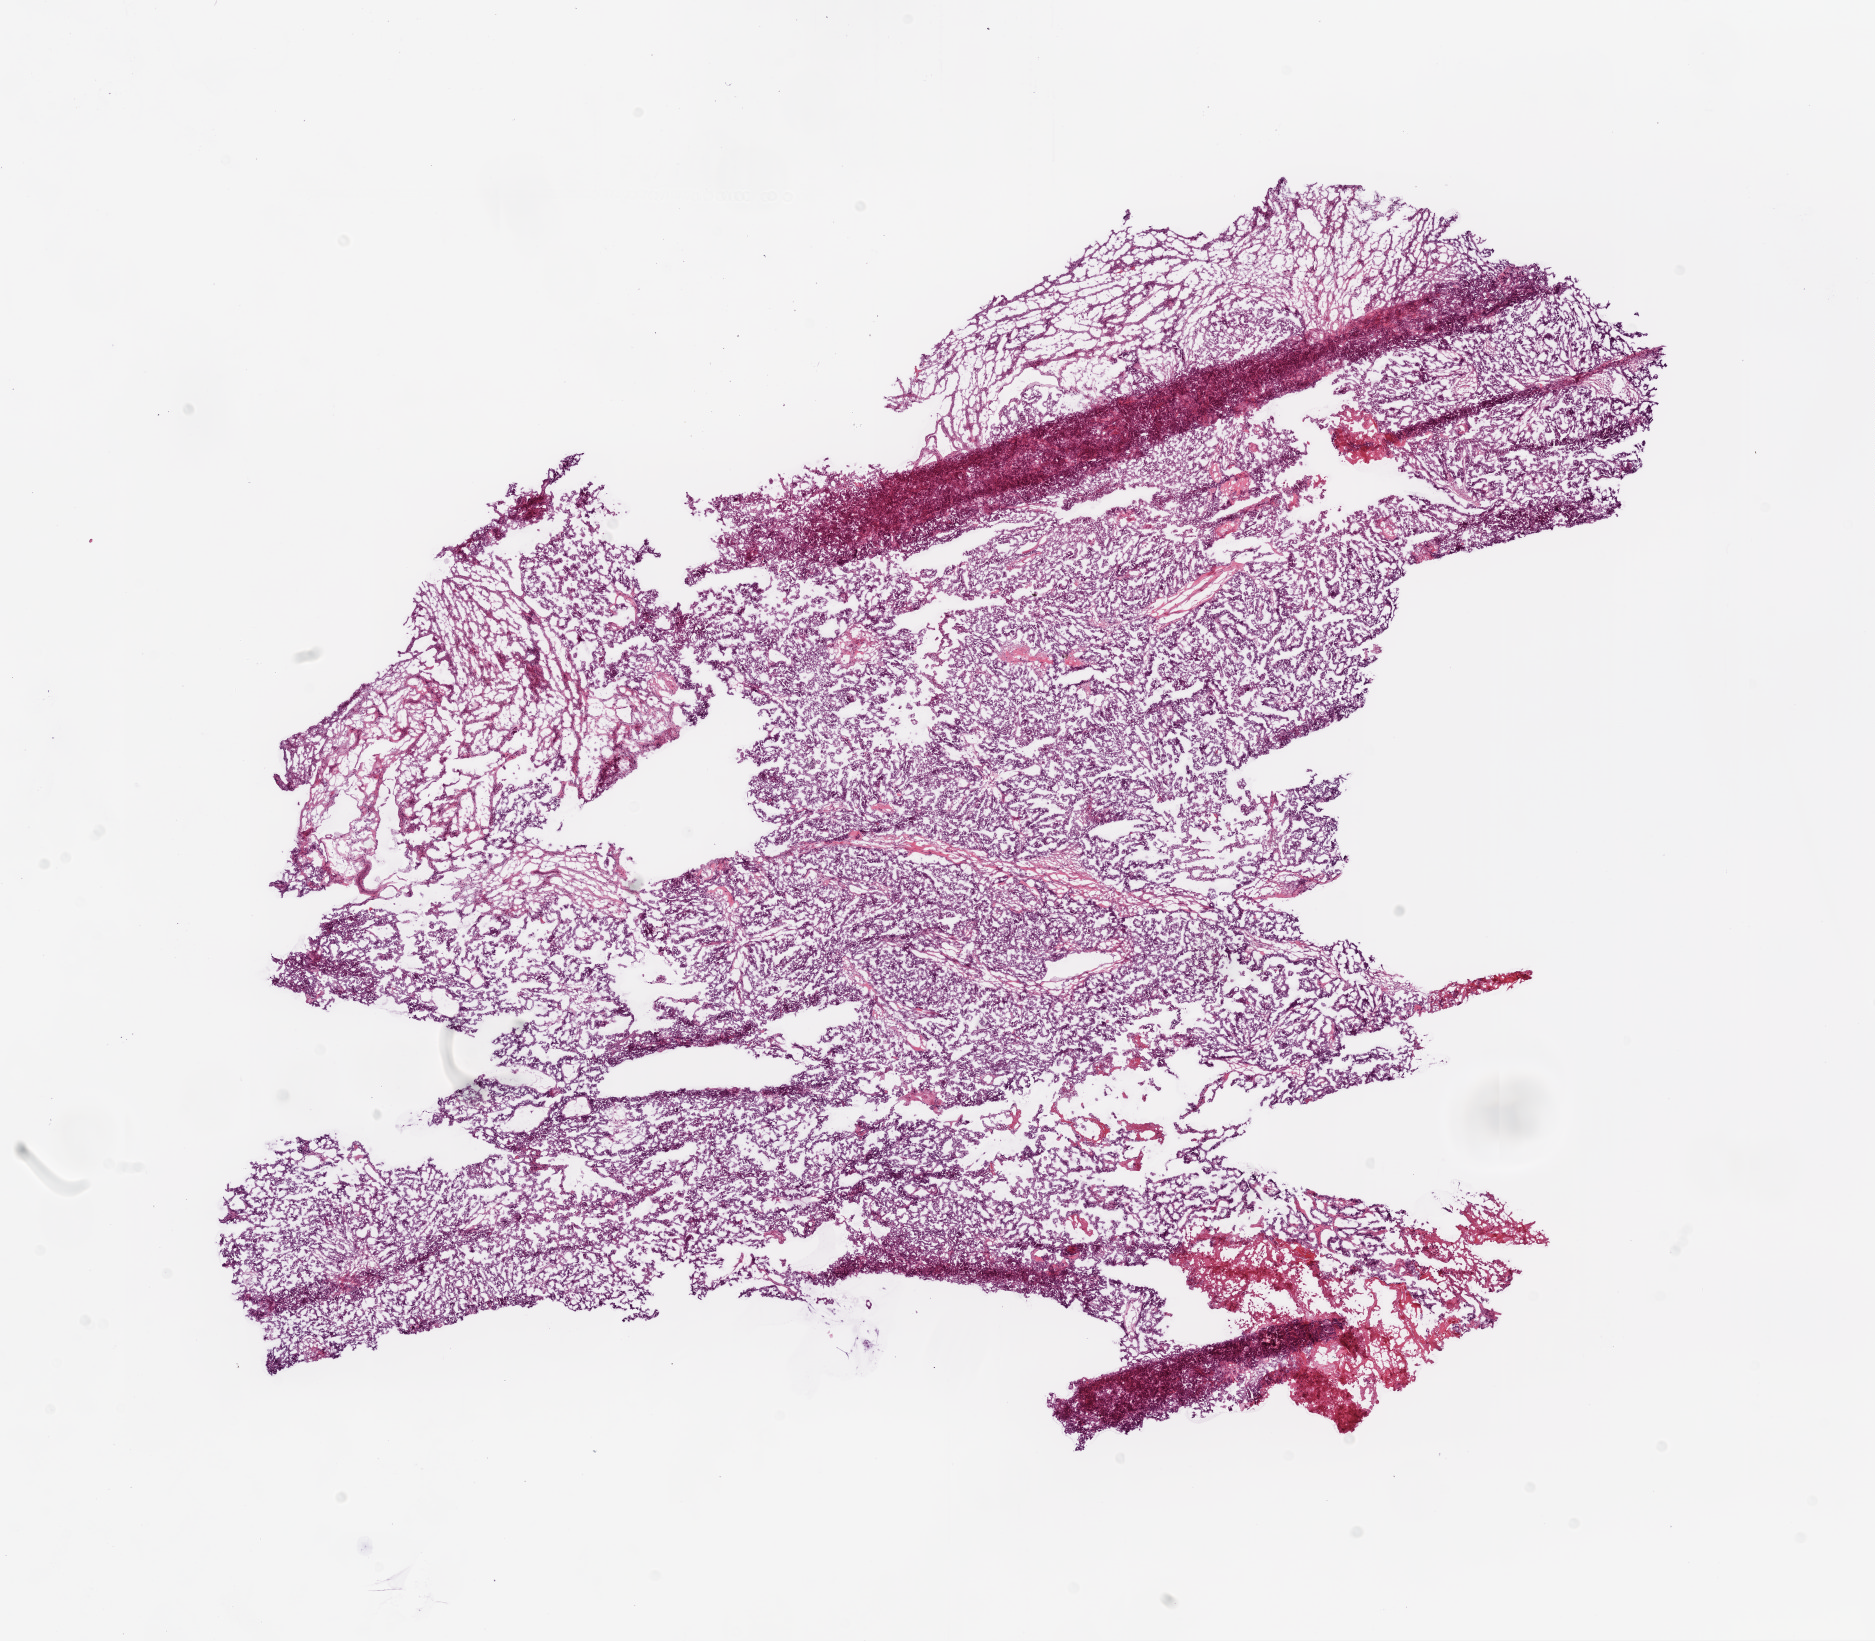
Digitized H&E tissue section (whole slide), low-resolution overview of the scanned area, about 15.0 x 13.2 mm (from a 20x scan); frozen section; ovary, primary tumour sample. Patient sex: female. Histologic grade: G3 (poorly differentiated). Pathologist review of this section (percent, as recorded): tumour cells 85%, tumour nuclei 80%, normal cells 0%, stromal cells 10%, necrosis 5%. Inflammatory infiltration, as recorded: lymphocyte infiltration 10%, monocyte infiltration 0%, neutrophil infiltration 0%.
Diagnosis: Serous cystadenocarcinoma, NOS. Laterality: left. FIGO stage: IIIC.